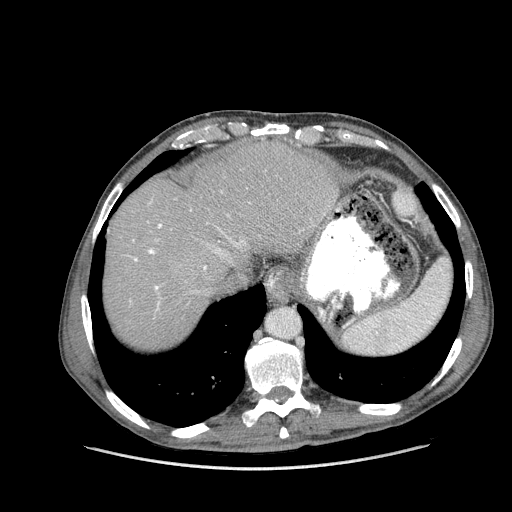
Contrast-enhanced abdominal CT (liver protocol), one axial slice. Soft-tissue window (W 400 / L 40 HU). 2.5 mm slice thickness. 512 × 512 image matrix, field of view 400 × 400 mm. From the clinical record (not read from this slice): diagnosis: hepatocellular carcinoma (patient treated with transarterial chemoembolisation; whether this scan precedes or follows treatment is not stated here); TNM stage (as recorded): Stage-IIIA; Child-Pugh class: A.
Structures marked on this image (semi-automatically segmented with operator editing):
- abdominal aorta: bounding box [x1, y1, x2, y2] px = [268, 308, 299, 338]
- liver parenchyma outside the tumour (the mass and vessels are separate outlines, so this box may not span the whole liver): [104, 142, 338, 348]
- liver vessels: [129, 201, 245, 310]